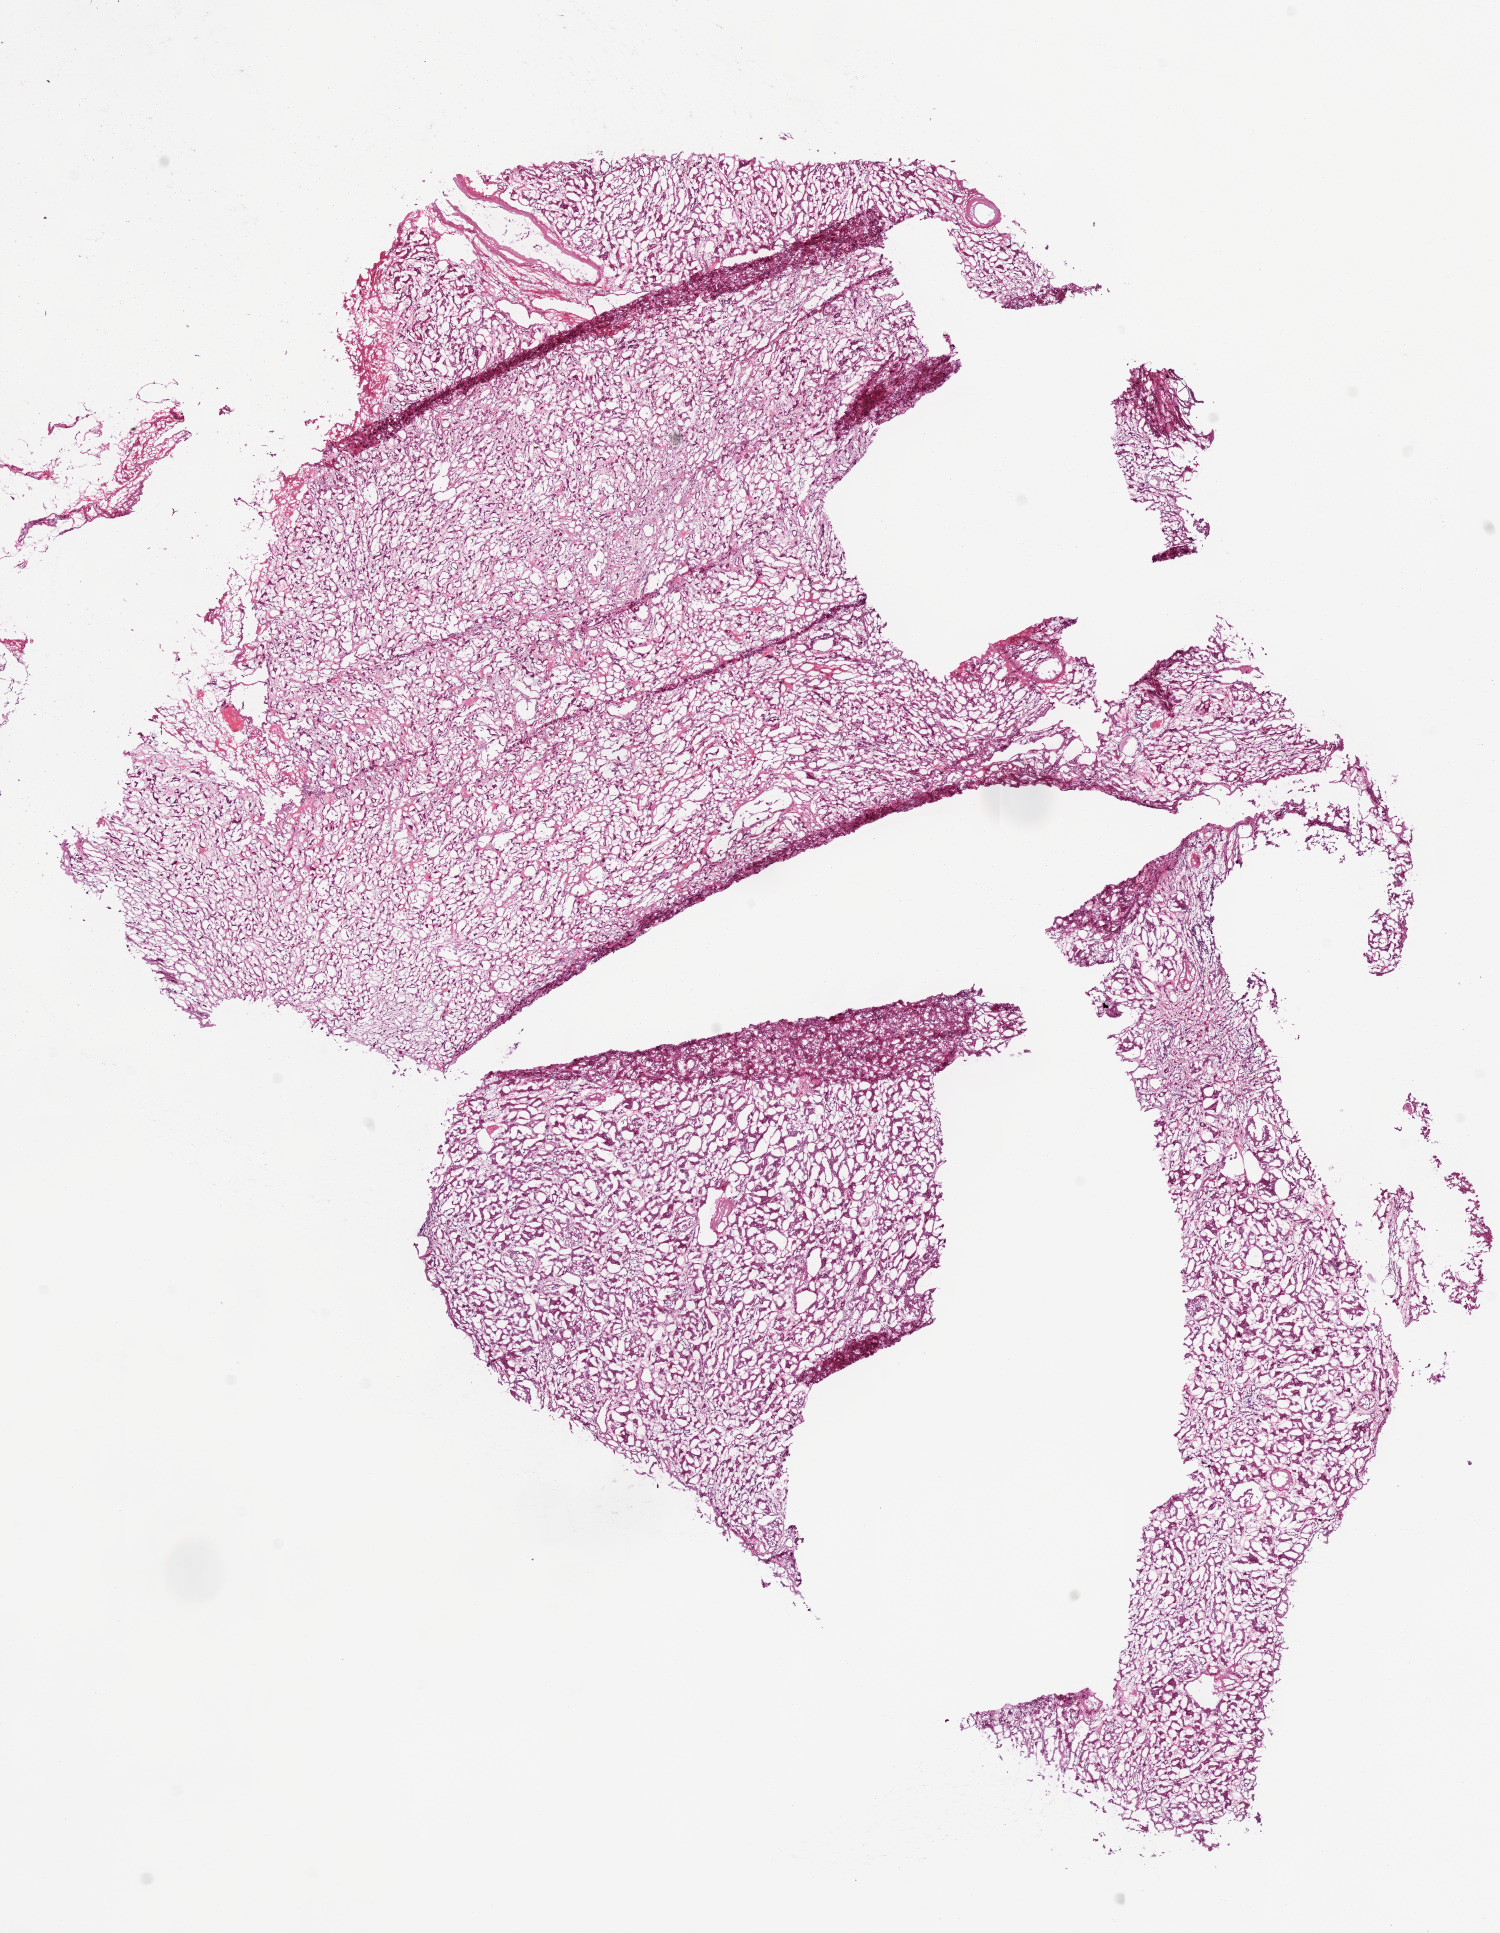
Whole-slide histology image, H&E — shown as a low-resolution overview of the whole scanned area (about 12.0 x 15.5 mm). Frozen section from the bottom of the tissue portion. Sample: solid tissue normal (non-tumour tissue), kidney. Female, age 64 years at initial diagnosis.
- this section: solid tissue normal (non-tumour) sample from the same patient
- patient diagnosis: Clear cell adenocarcinoma, NOS